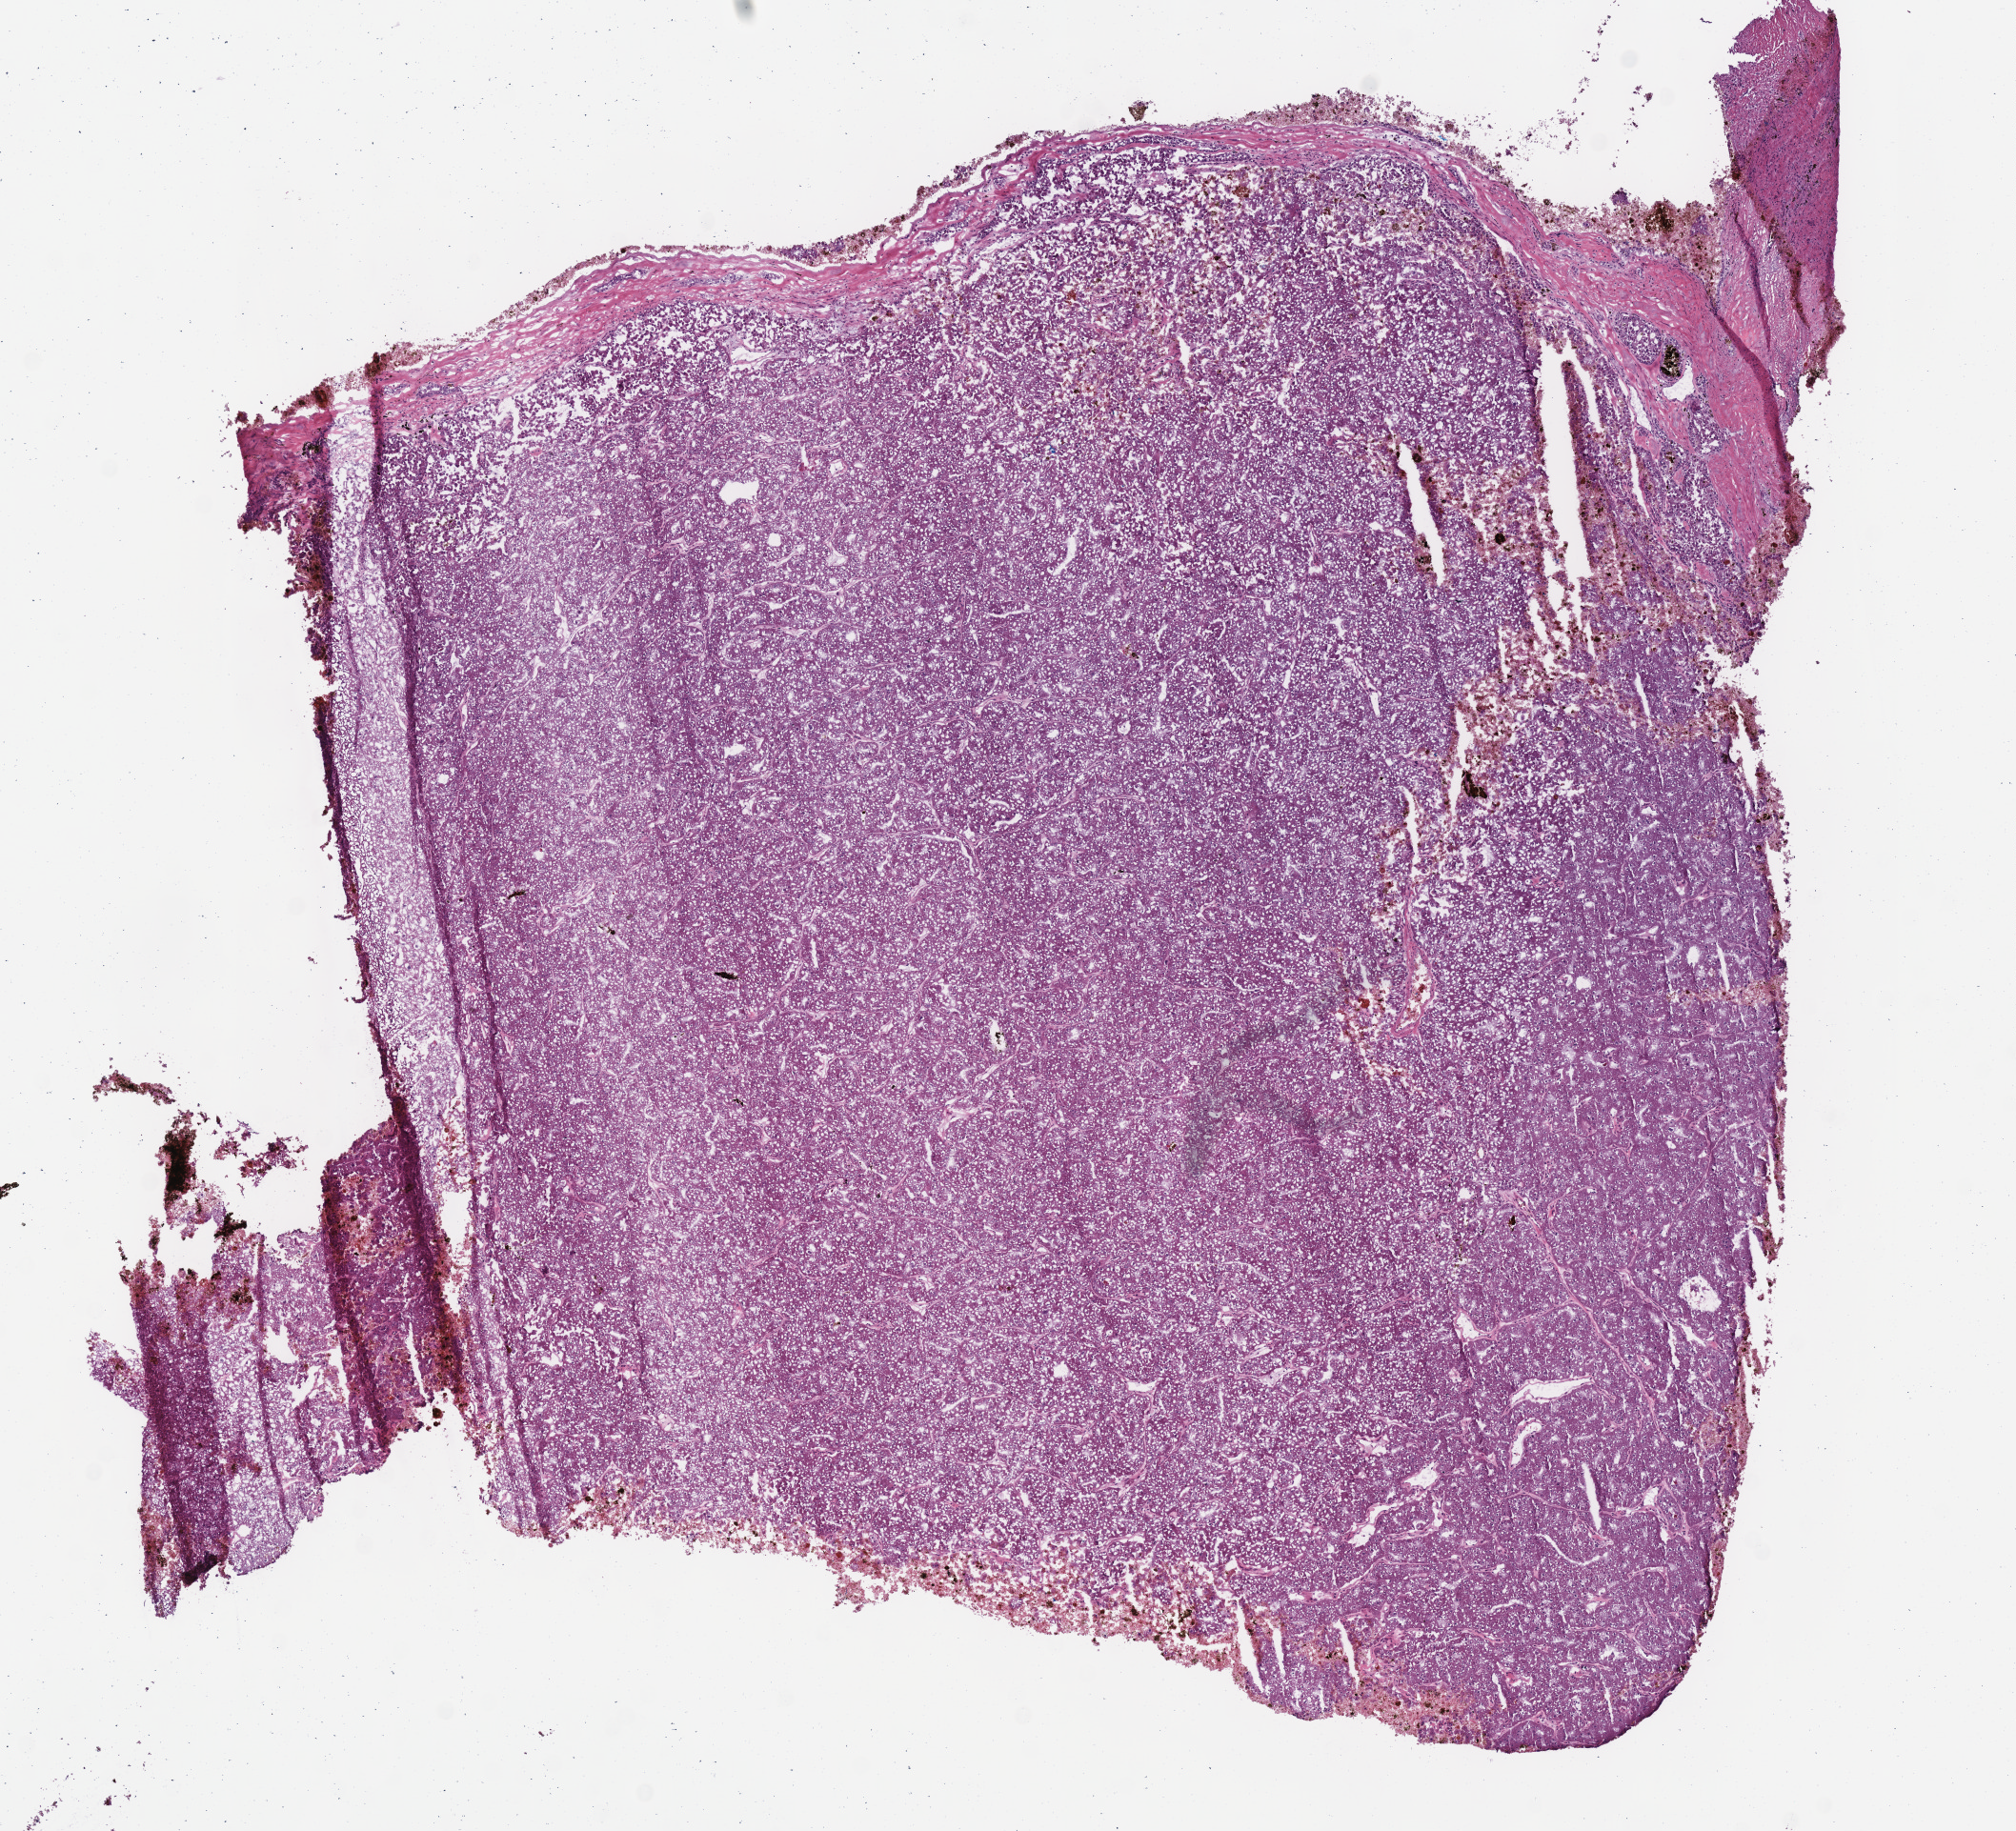
Hematoxylin and eosin (H&E) stained whole-slide image, shown as a low-resolution overview of the whole scanned area (about 8.3 x 7.6 mm, slide scanned at 40x), frozen section from the top of the tissue portion, kidney, primary tumour sample. Male, age 56 years at initial diagnosis. Slide review estimates, as recorded: tumour cells 90%, tumour nuclei 92%.
Pathologic diagnosis: Renal cell carcinoma, chromophobe type.